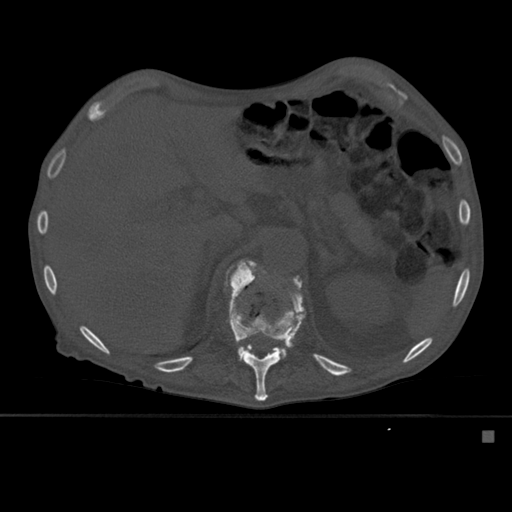
CT including the spine, one axial slice; slice 272 of 527 in the series (ordered by position); bone window (W 1800 / L 400 HU); 1.5 mm slice thickness; 512 × 512 image matrix, field of view 373 × 373 mm. Patient: male, 78 years. Case-level facts recorded for this patient, not image findings: primary cancer: prostate.
Structures marked on this image (semi-automatic segmentation, software-assisted and operator-edited):
- L1 vertebra: bounding box [x1, y1, x2, y2] px = [238, 261, 286, 356]
- T12 vertebra: [225, 259, 306, 401]